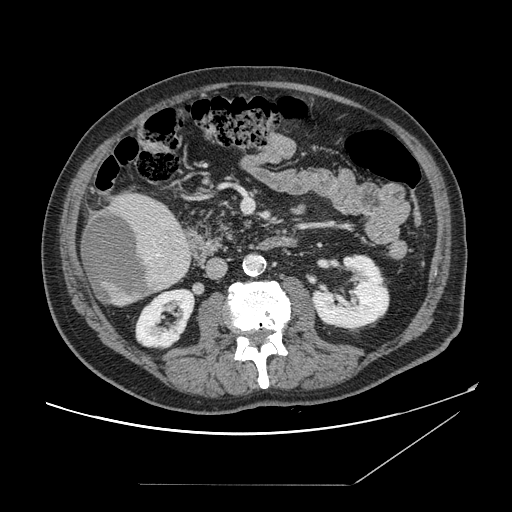
Contrast-enhanced abdominal CT, one axial slice; 120 kVp; intravenous contrast given; soft-tissue window (W 400 / L 40 HU); 2.5 mm slice thickness; 512 × 512 image matrix, field of view 416 × 416 mm. Male patient, age 80 years. Case-level facts recorded for this patient, not image findings: diagnosis: colorectal cancer liver metastases, imaged before liver resection; multiple liver metastases: no; largest metastasis: 2.2 cm; disease in both lobes: no.
Annotated regions visible in this slice (outlined manually by an expert reader):
- liver: box from (x=81, y=193) to (x=191, y=306) px
- liver metastasis: (x=82, y=210)–(x=152, y=302)